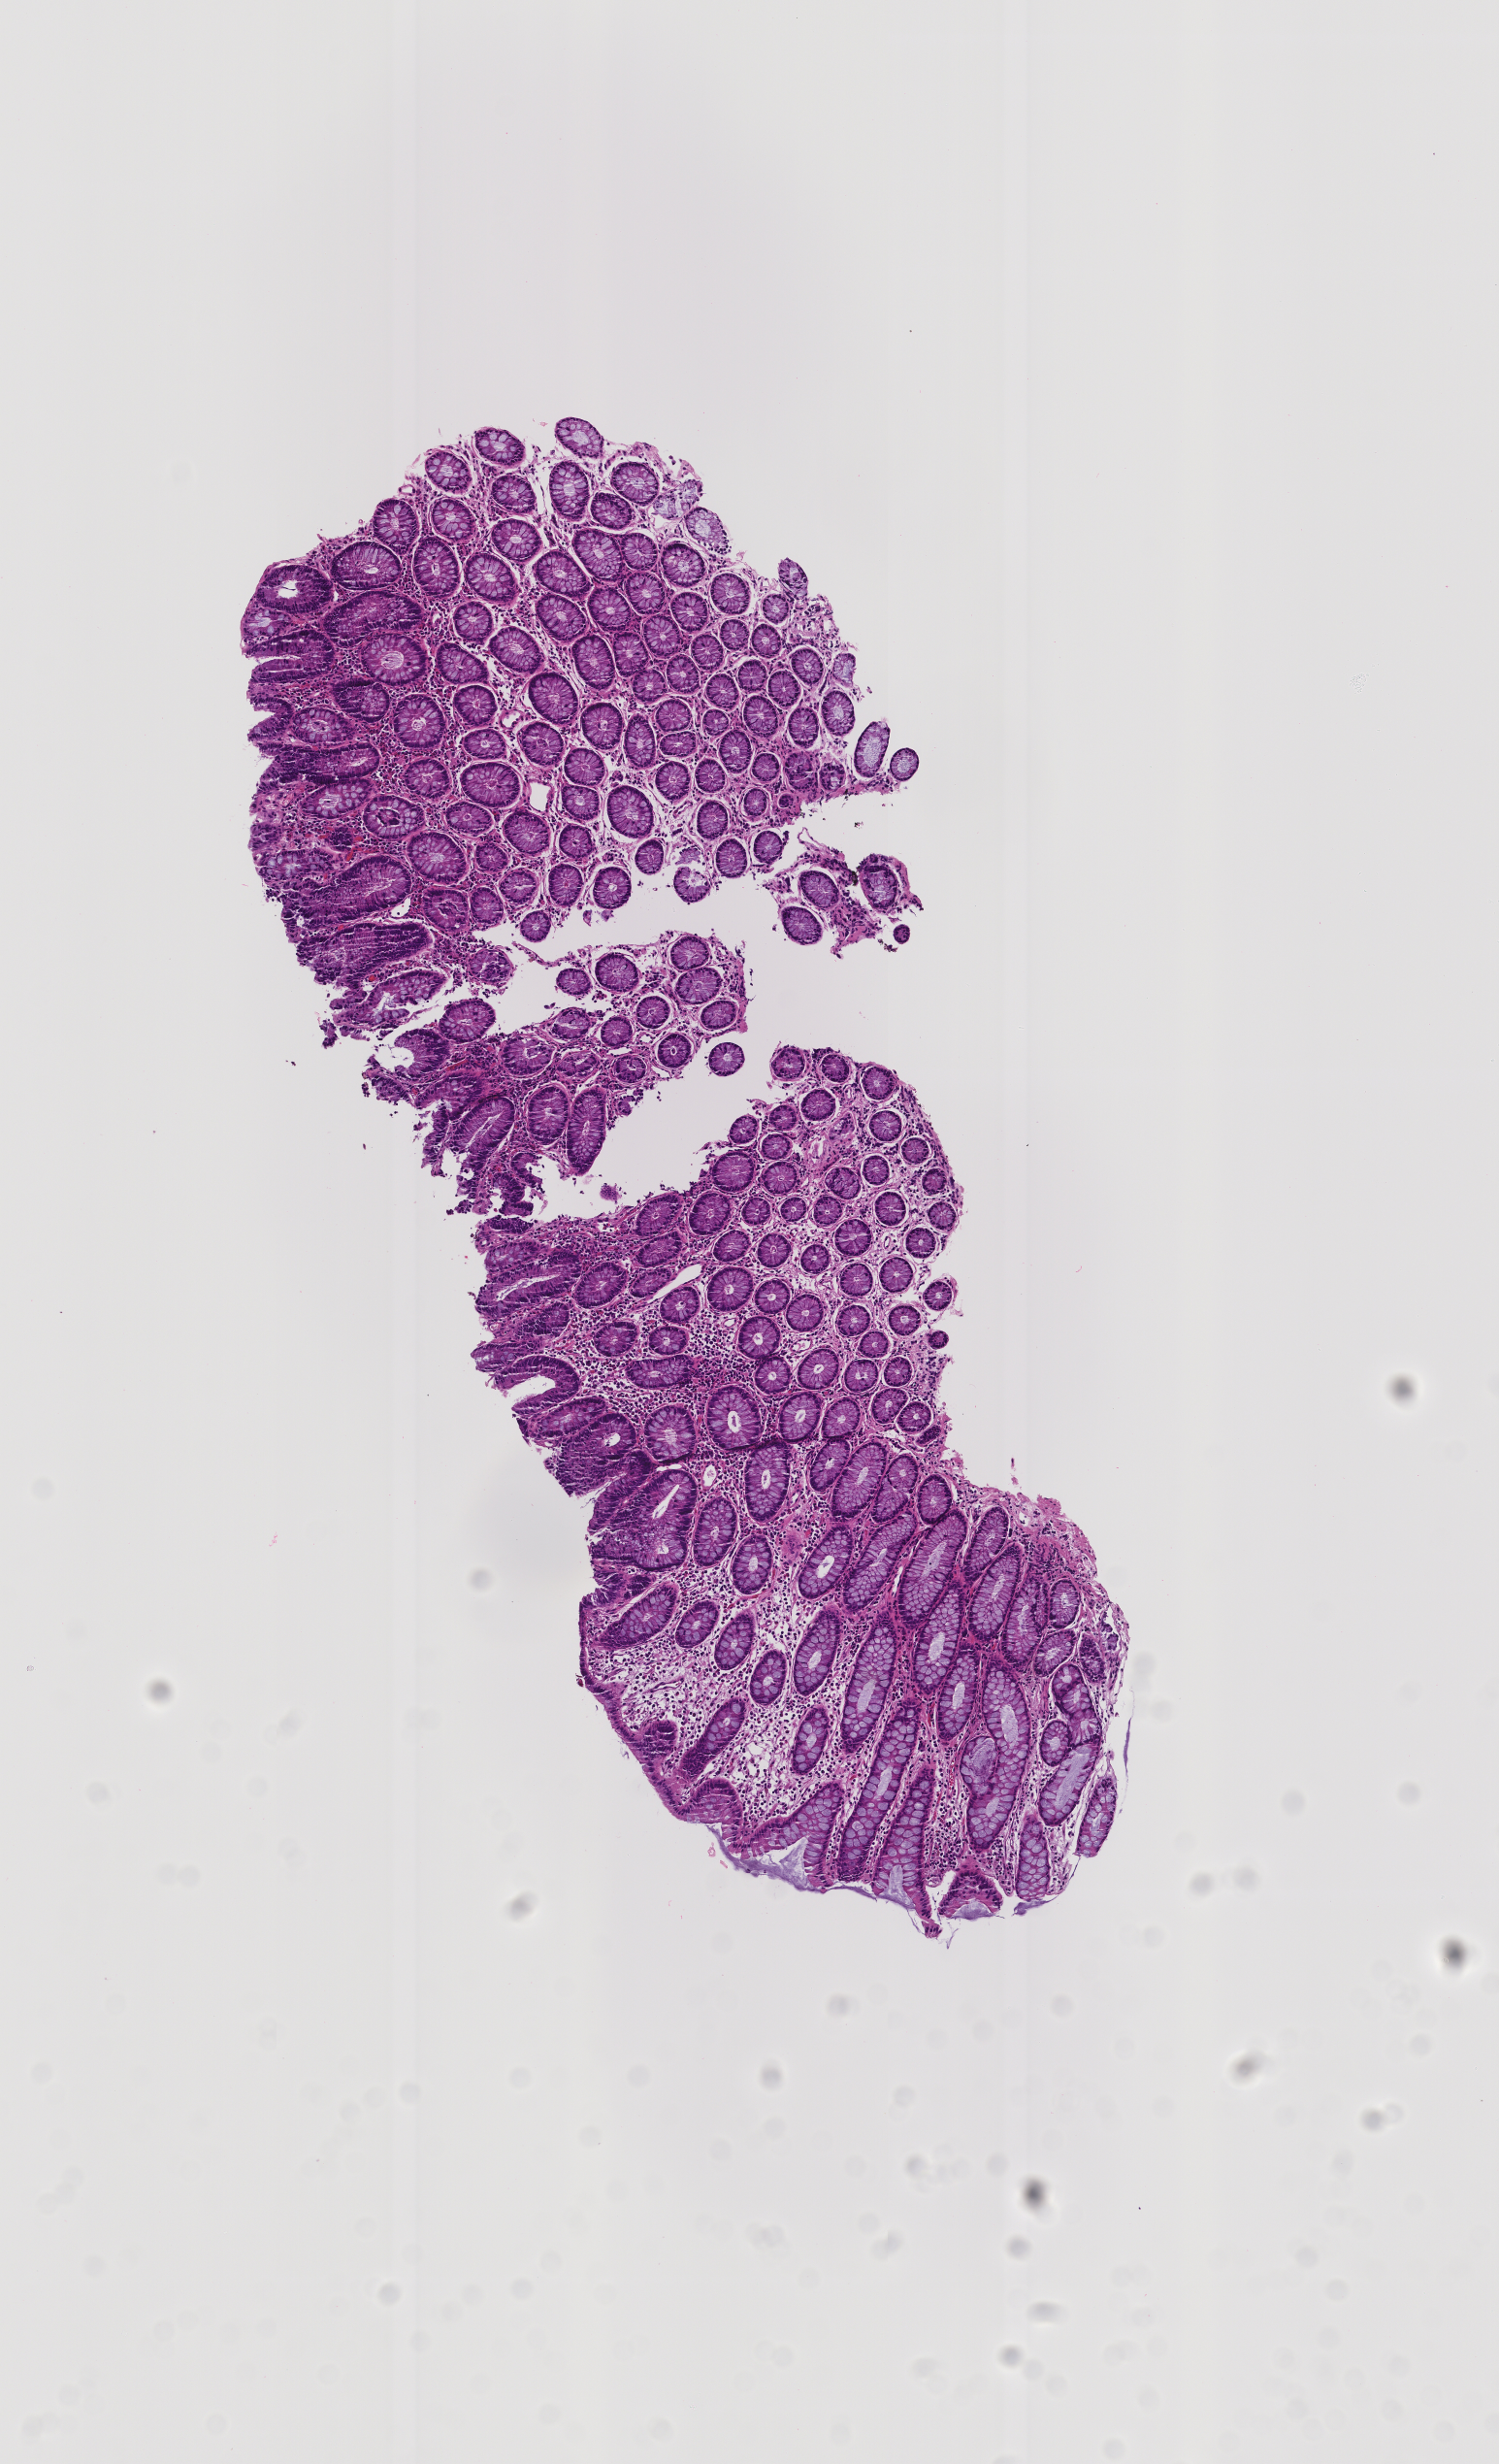
Whole-slide image, H&E stain: colon biopsy — low-resolution overview of the scanned area, about 3.1 x 5.1 mm; FFPE section; site: sigmoid colon. Patient: male.
Lesion category (as recorded): premalignant.